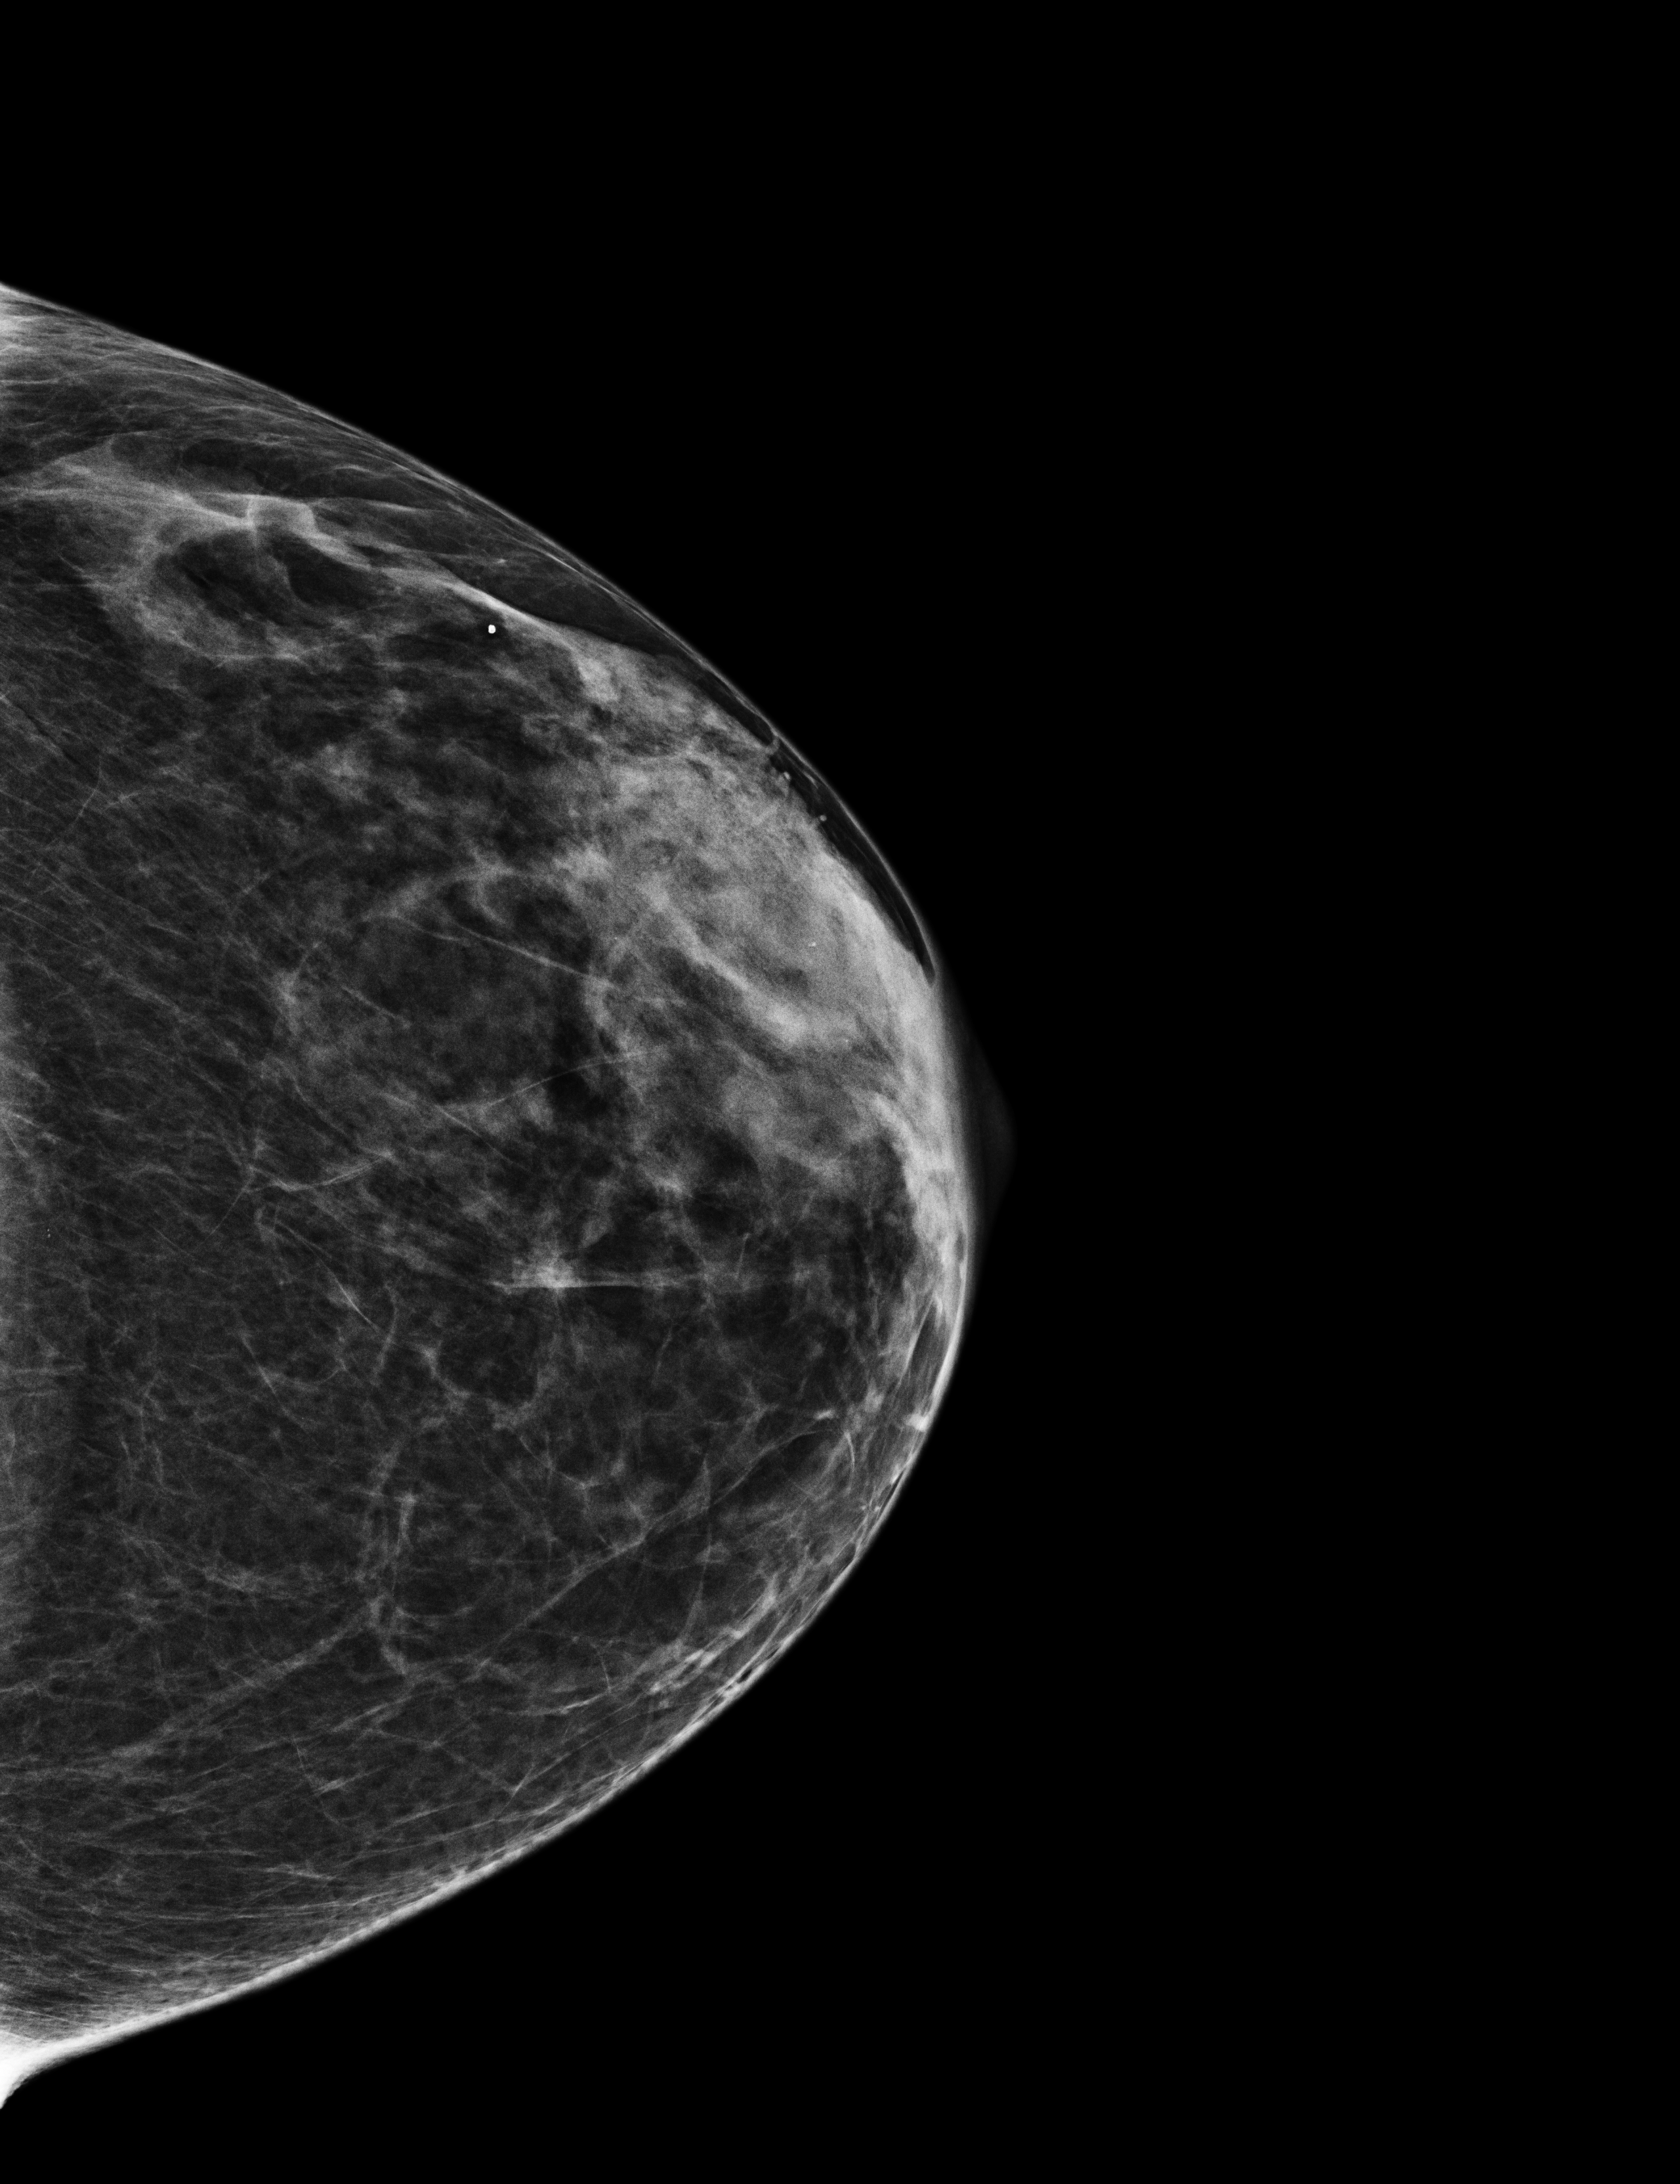
Diagnostic work-up study, system: Selenia Dimensions.
Image type: full-field digital mammogram. Breast: left. Projection: CC view.